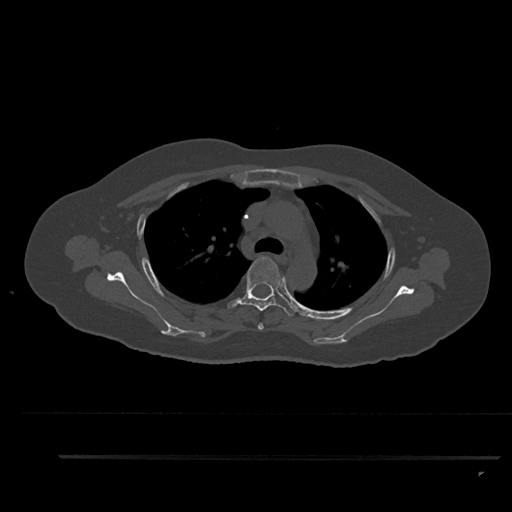
CT including the spine, one axial slice. Position 649 of 797 along the scan axis. 120 kVp. Bone window (W 1800 / L 400 HU). 0.5 mm slice thickness. 512 × 512 image matrix, field of view 408 × 408 mm. Patient: female, 44 years. From the clinical record (not read from this slice): primary cancer: renal; vertebrae with lytic lesions (as recorded): L1.
Annotated regions visible in this slice (semi-automatic segmentation, software-assisted and operator-edited):
- T3 vertebra: box from (x=258, y=323) to (x=264, y=330) px
- T4 vertebra: (x=227, y=257)–(x=296, y=316)